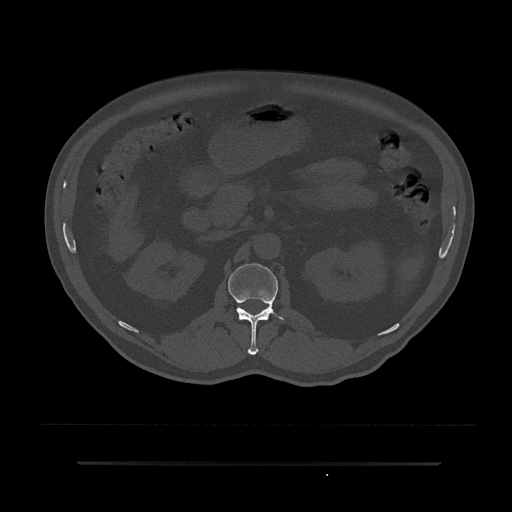
CT including the spine, one axial slice. Slice 139 of 797 in the series (ordered by position). 120 kVp. Bone window (W 1800 / L 400 HU). 0.5 mm slice thickness. 512 × 512 image matrix, field of view 464 × 464 mm. Male patient, age 59 years. Case-level facts recorded for this patient, not image findings: primary cancer: bile ducts.
Structures marked on this image (semi-automatic segmentation, software-assisted and operator-edited):
- L1 vertebra: bounding box <228,264,284,355> (left, top, right, bottom; pixels)